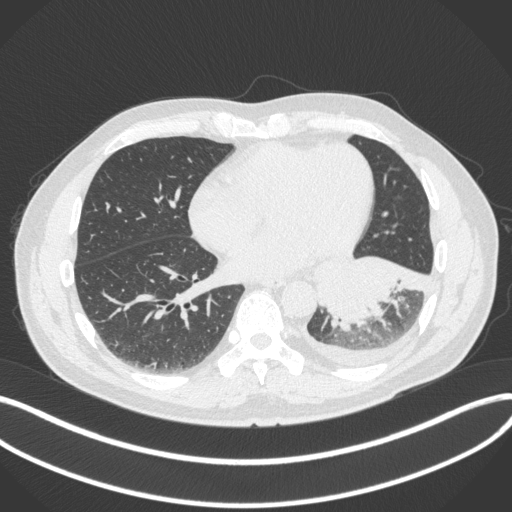
Chest CT, one axial slice. Slice 135 of 350 in the series (ordered by position). Reconstruction kernel B31f. 120 kVp. Lung window (W 1500 / L -600 HU). 1 mm slice thickness. 512 × 512 image matrix. Patient: male, 58 years. Case-level facts recorded for this patient, not image findings: clinical TNM (as recorded): T3 N1 M1b; histopathological grade: G3.
Structures marked on this image (bounding box drawn by a radiologist):
- lung tumour (recorded histology: small cell carcinoma): bounding box [x1, y1, x2, y2] px = [311, 250, 426, 332]